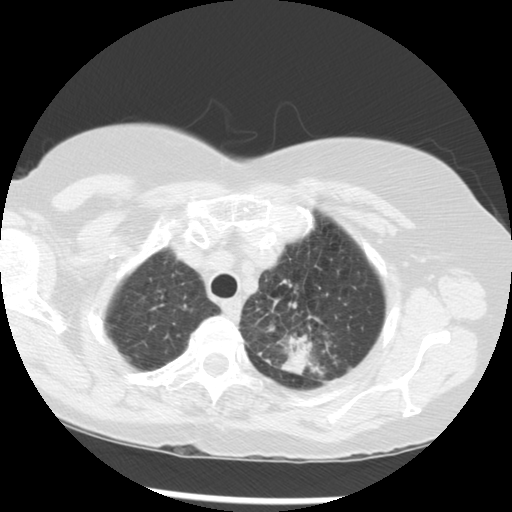
Low-dose screening chest CT, axial slice; third screening round (two years after baseline); lung window (W 1500 / L -600 HU); 2.5 mm slice thickness; slice 240 of 283 in the series. Female participant, aged 70 years at enrolment. Current smoker at enrolment.
Lesion marked by an expert reader, box from (x=249, y=289) to (x=347, y=377) px. The exam's reader record, not a measurement of the box and not confirmed to be the same lesion: non-calcified nodule or mass ≥4 mm, left upper lobe, 32 × 26 mm, spiculated (stellate) margins, soft tissue attenuation, pre-existing on the prior screen: yes; interval growth: yes. Lung cancer was diagnosed 24 days after this screen: neoplasm, malignant, left upper lobe, stage IIIB (AJCC 6th edition), 40 mm at pathology.